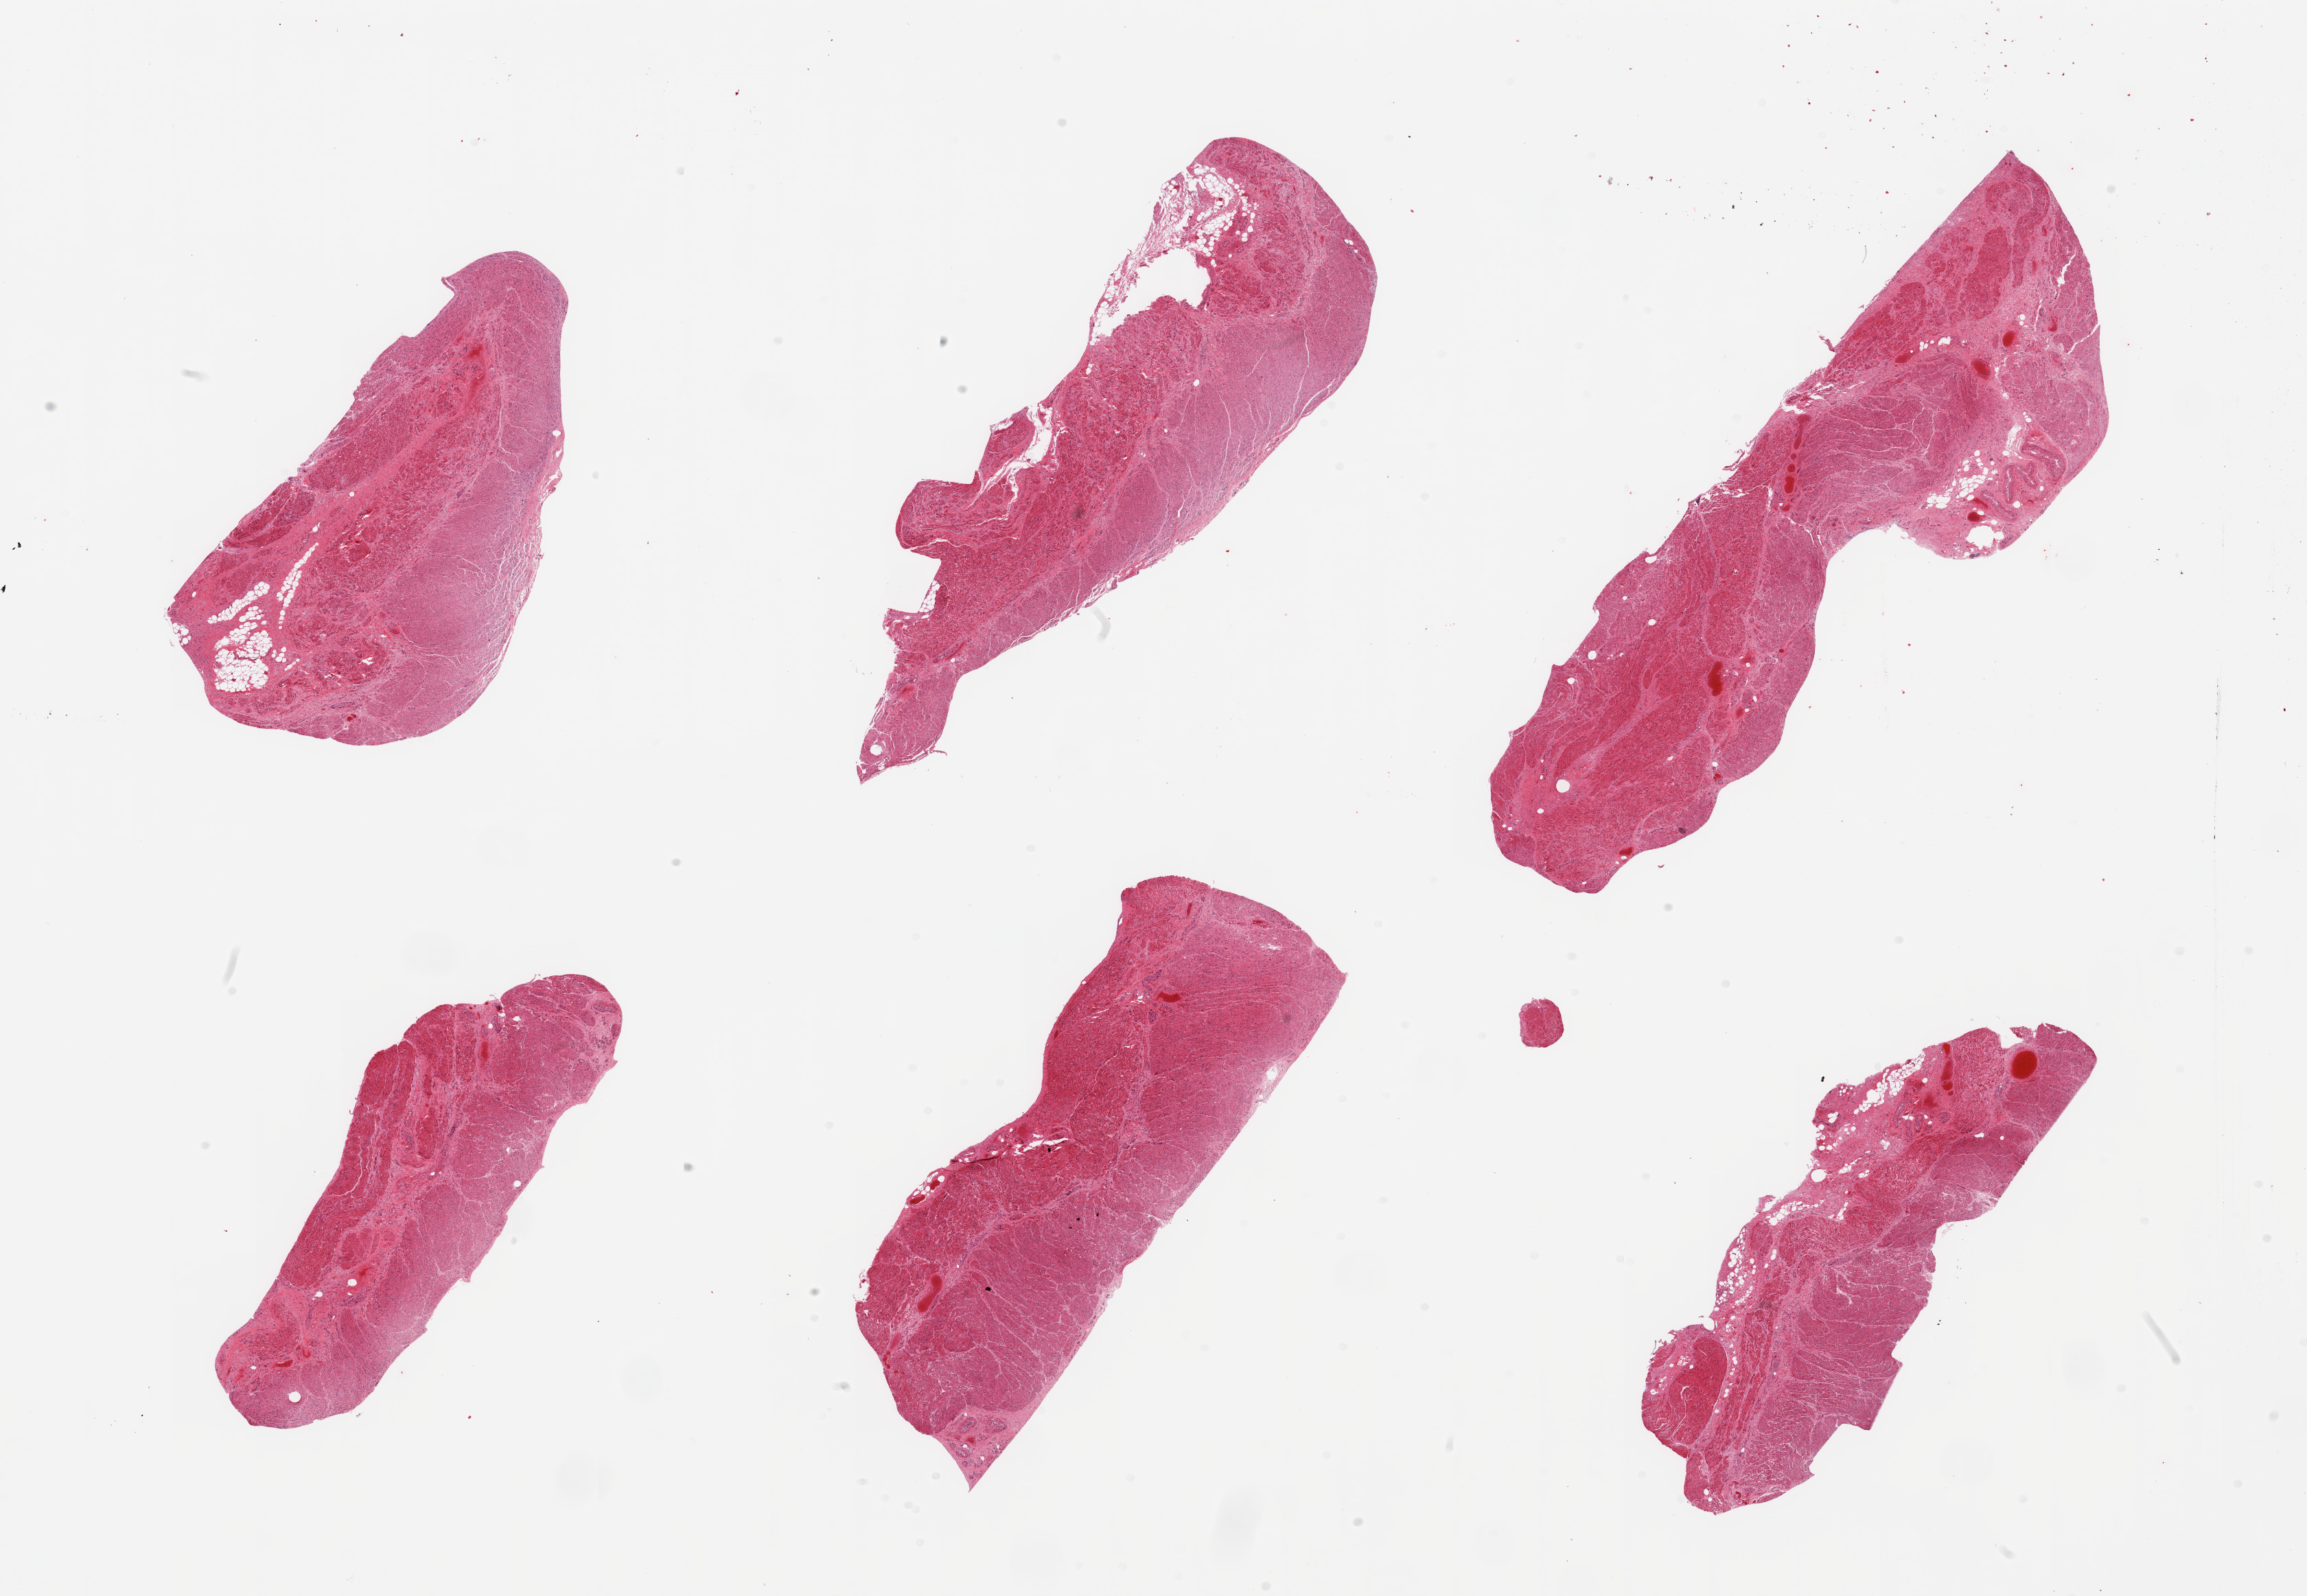
Digitized haematoxylin and eosin-stained section, whole scanned area (about 26.6 x 18.4 mm) shown as a low-resolution overview. PAXgene-fixed paraffin-embedded (PFPE) section. Target tissue: gastroesophageal junction. Tissue donor sample.
Review note (as recorded): 6 pieces; target muscularis, some residual attached fat.